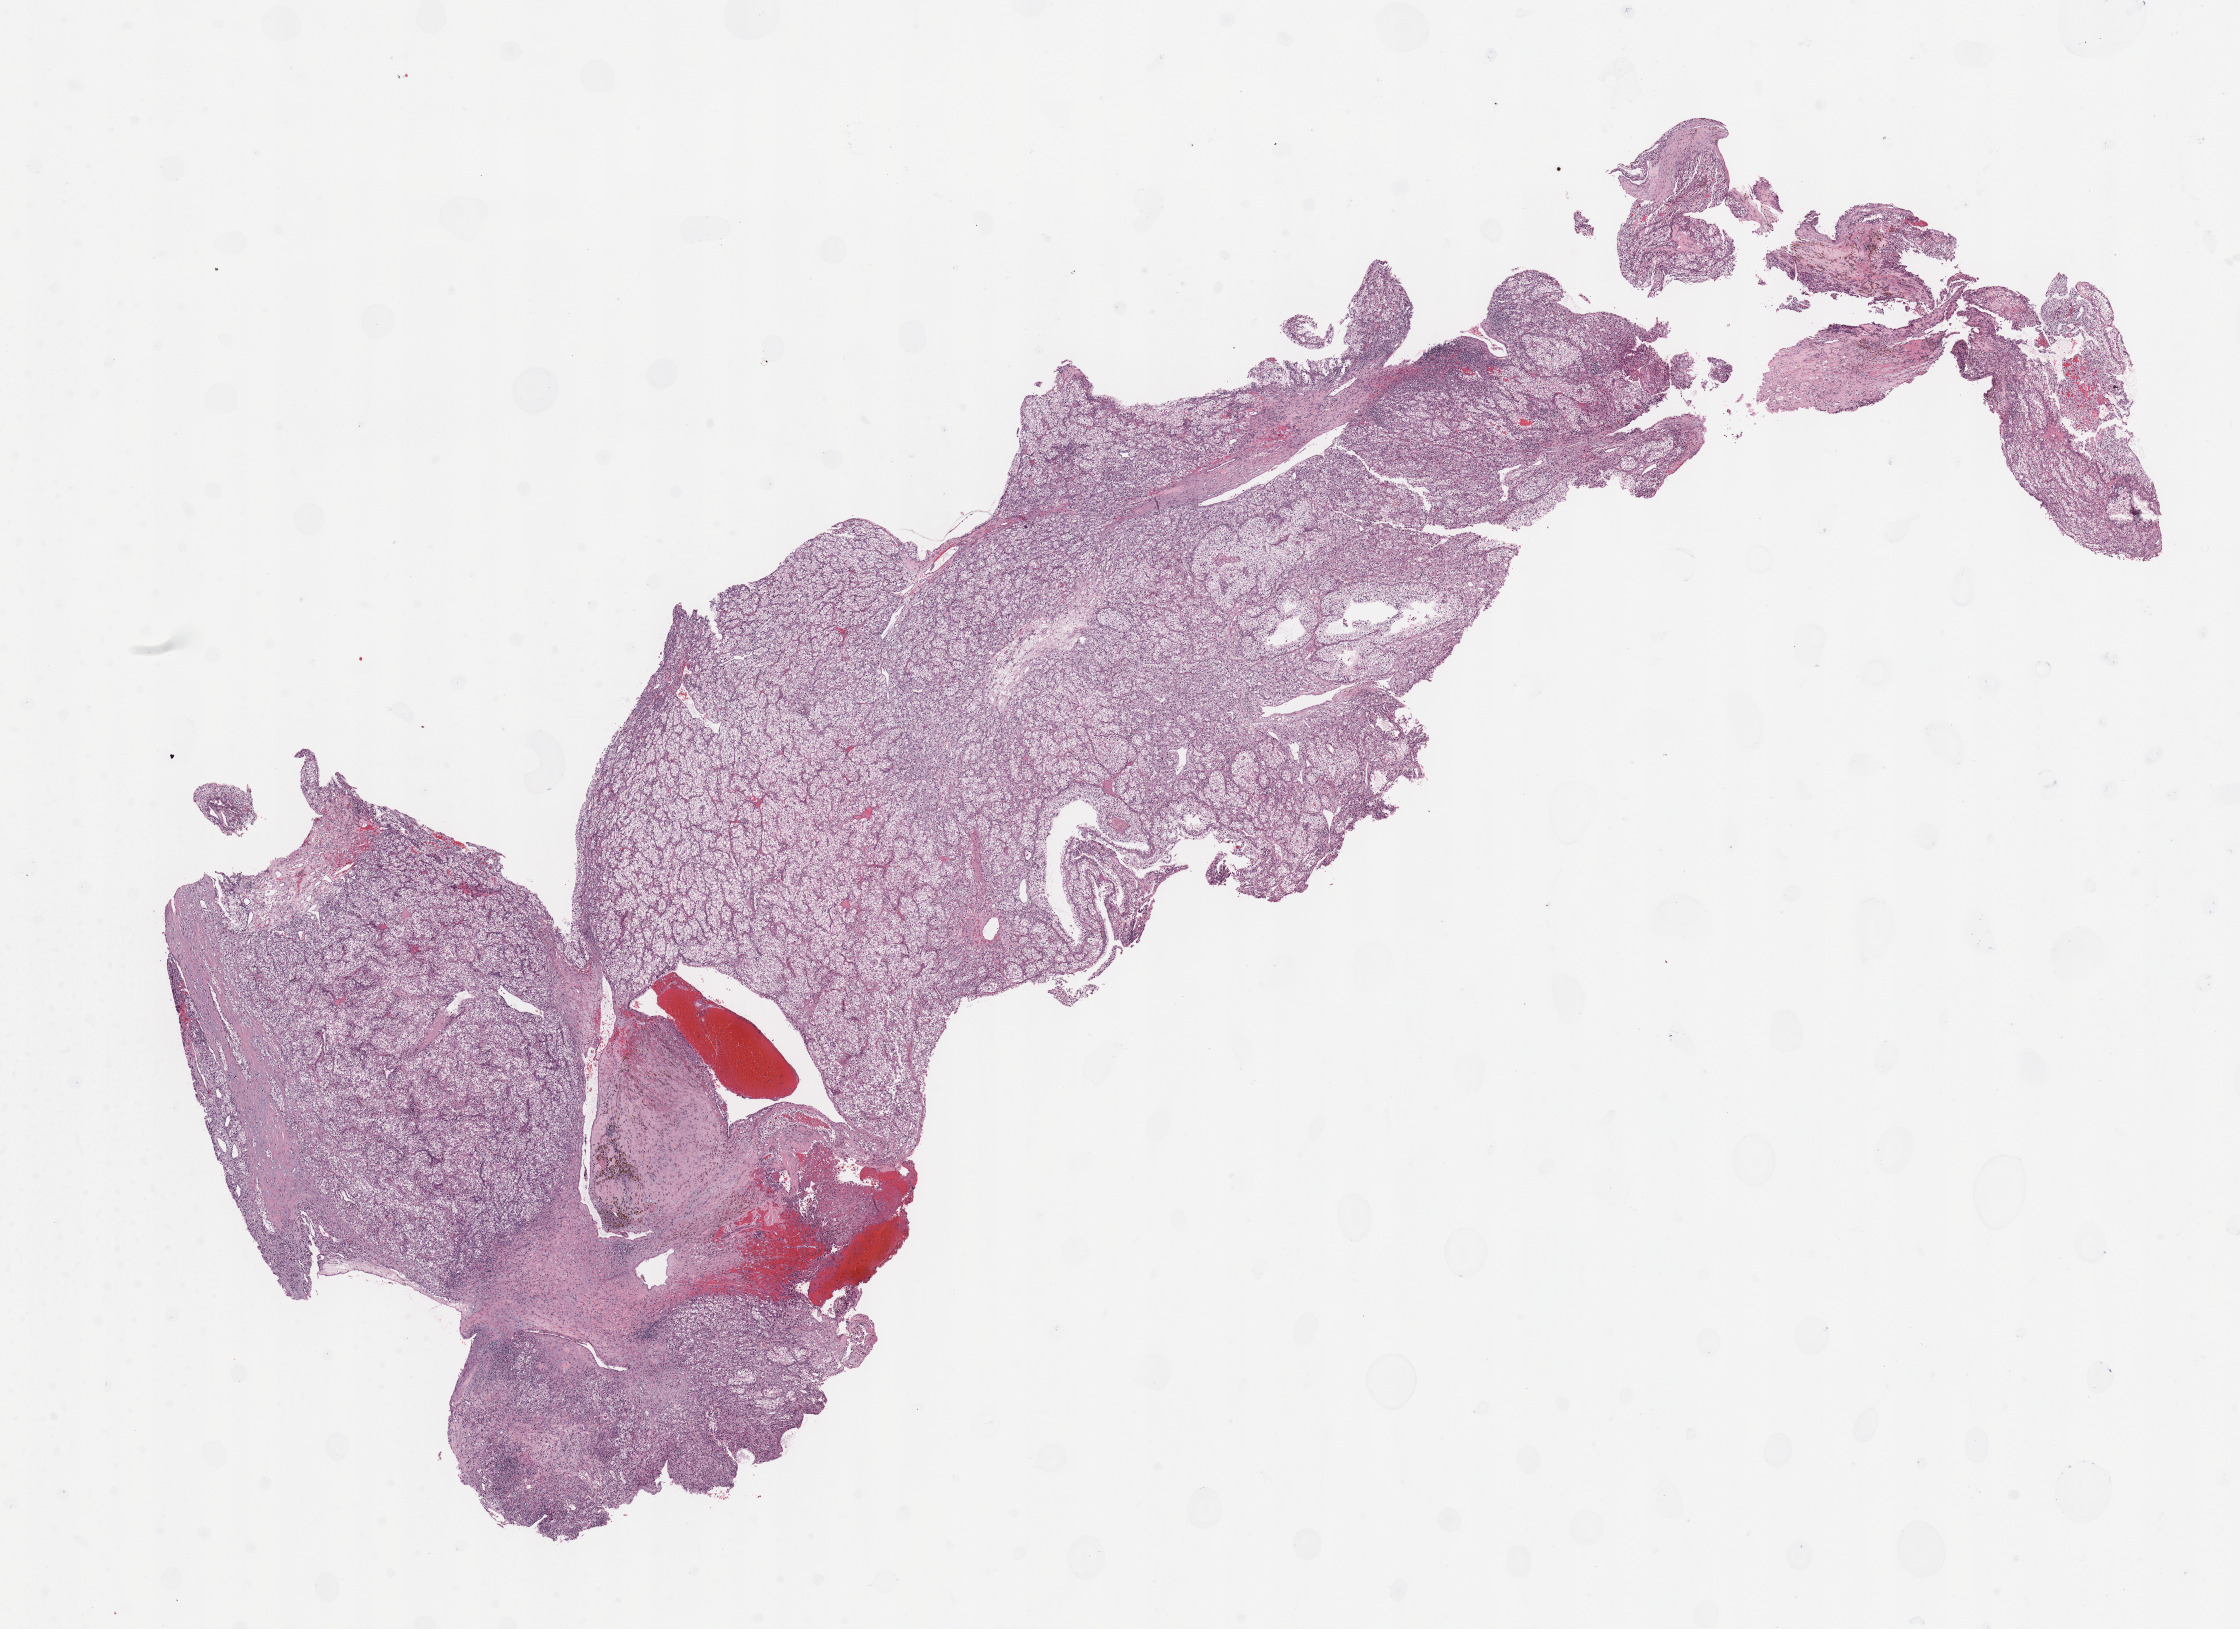
Digitized H&E-stained tissue section (whole slide), whole scanned area (about 17.7 x 12.9 mm, from a 20x scan) shown as a low-resolution overview, tumour tissue sample, sampled site: kidney. 53-year-old male patient. Histologic grade: G3 (poorly differentiated). Pathologist review of this section (percent, as recorded): tumour nuclei 85%, necrosis 2%.
AJCC pathologic stage: II. Diagnosis: Renal cell carcinoma, NOS. Primary tumour site (as recorded): middle.